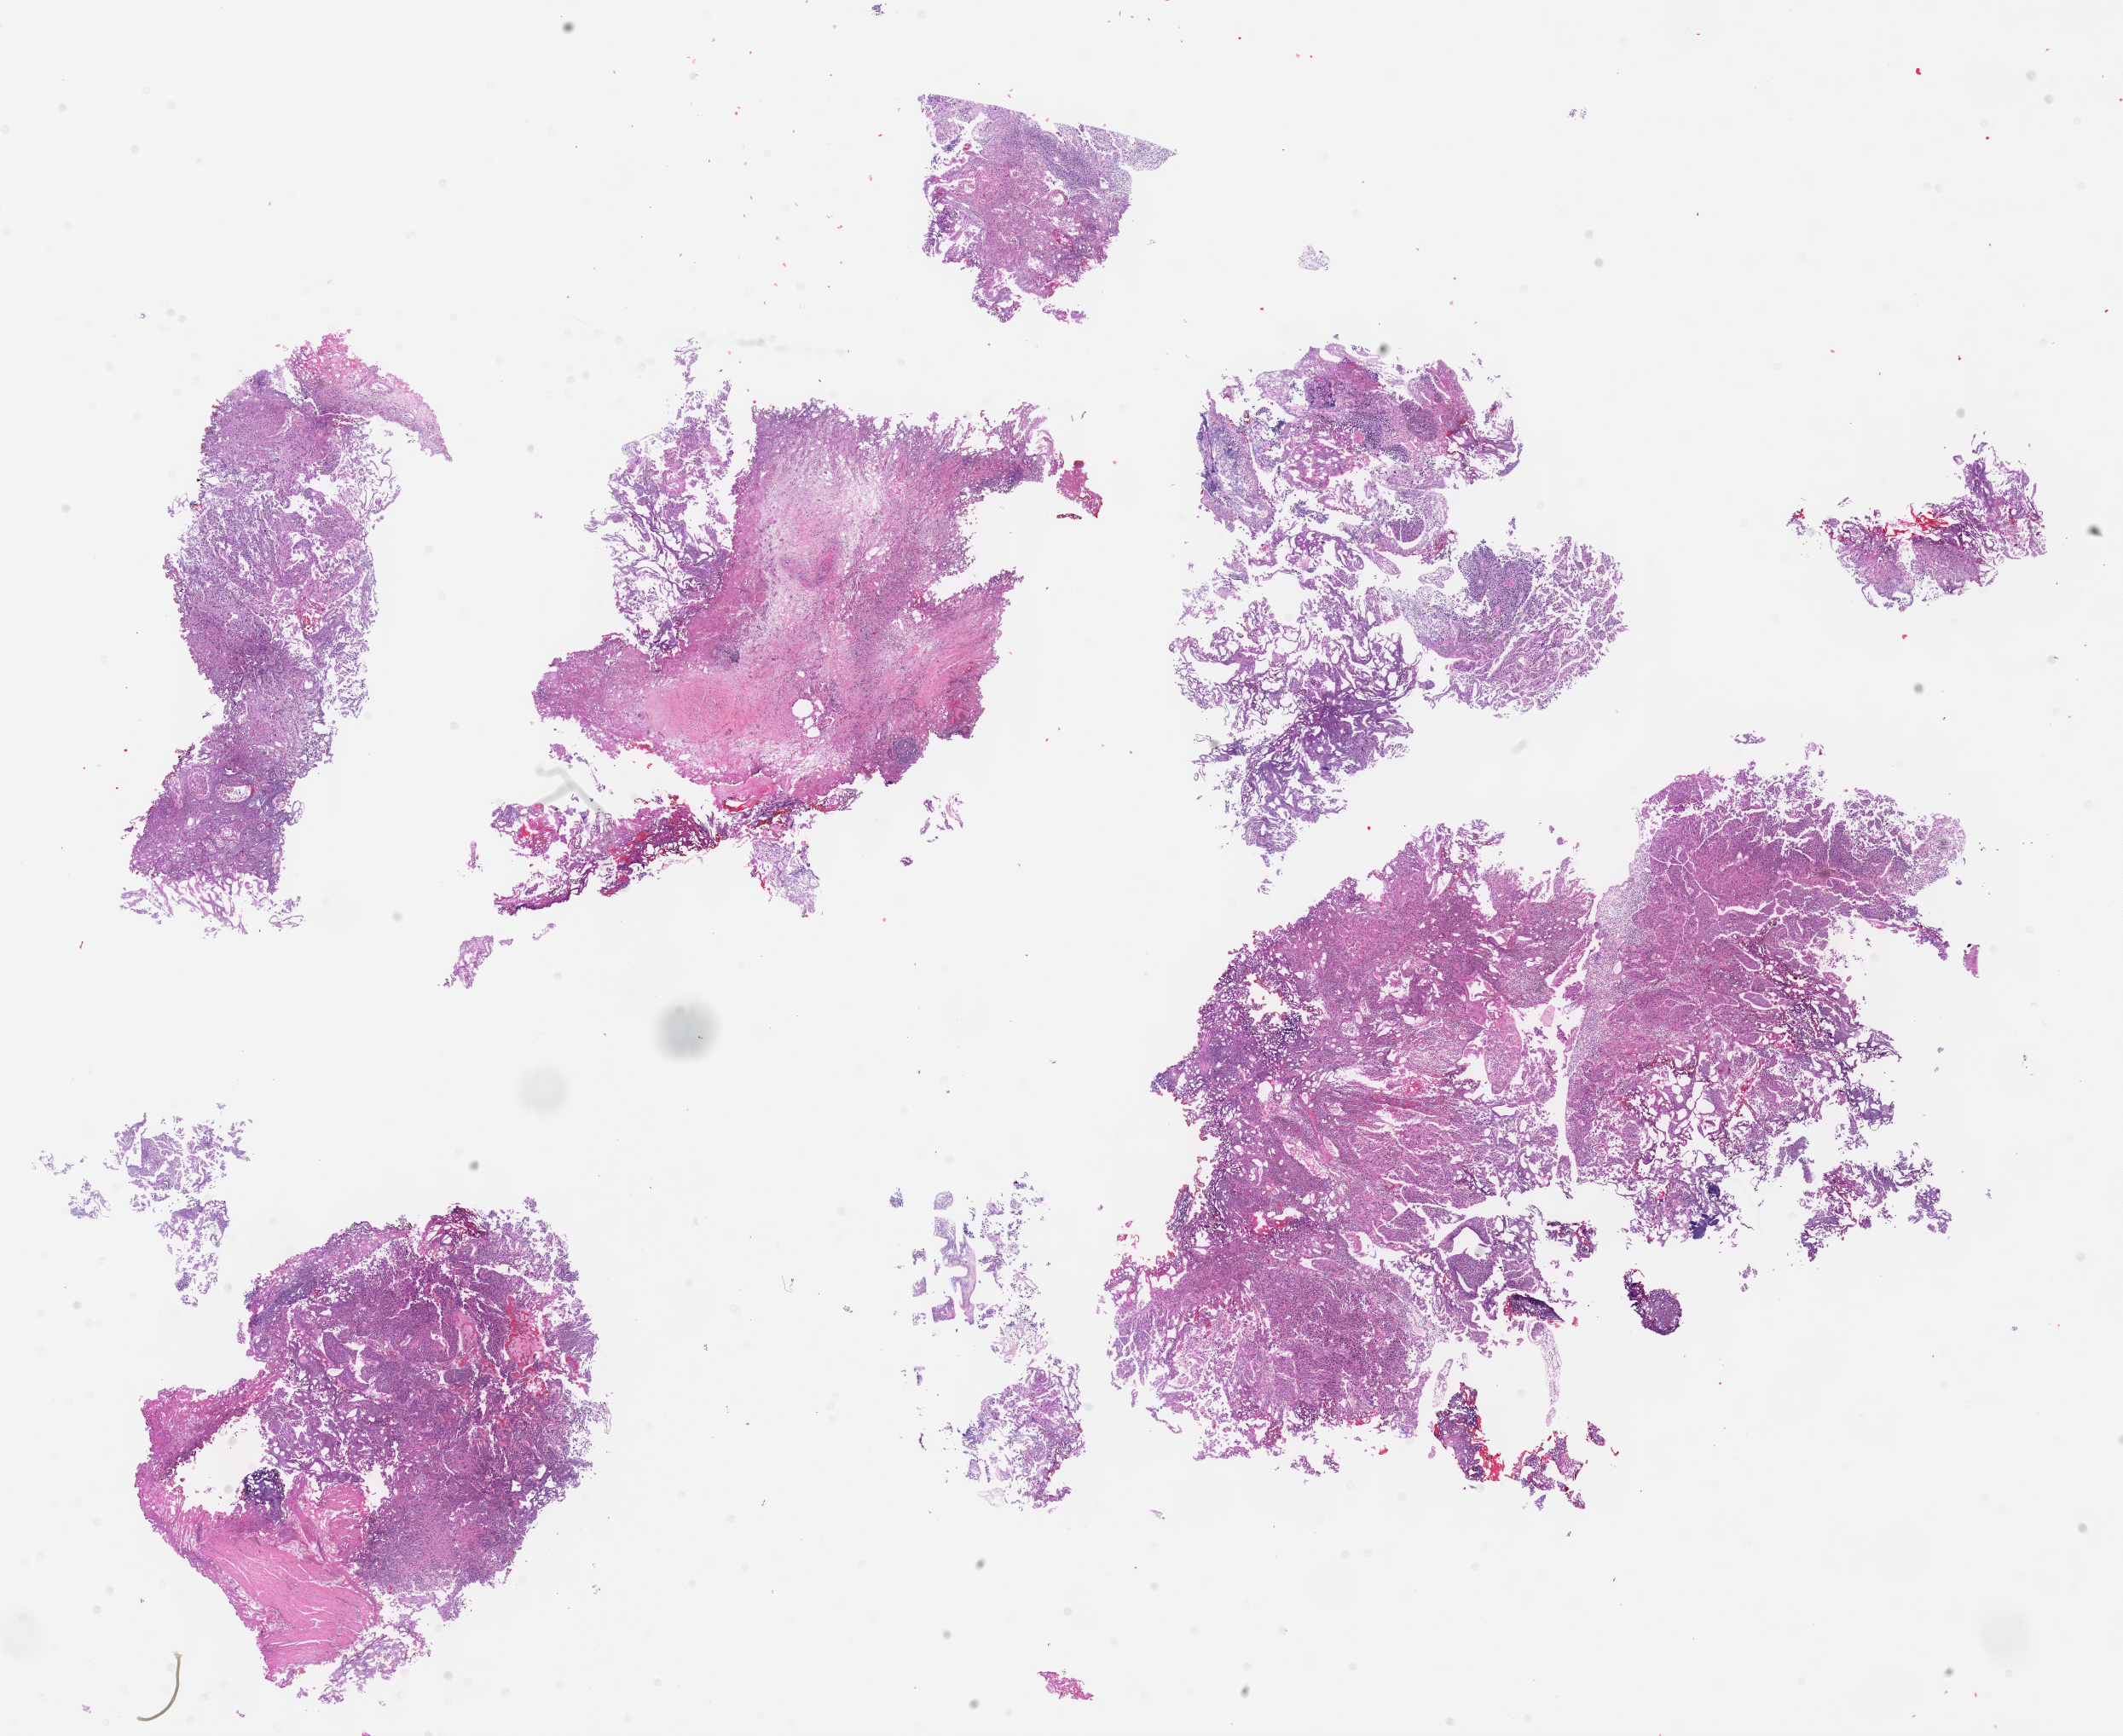
Whole-slide histology image, H&E-stained — whole scanned area (about 20.1 x 16.5 mm) shown as a low-resolution overview, formalin-fixed paraffin-embedded (FFPE) diagnostic section, sample: primary tumour, bladder. Female patient; age at initial diagnosis 75 years. Histologic grade: high grade.
AJCC pathologic stage: II. Histologic diagnosis: Transitional cell carcinoma.